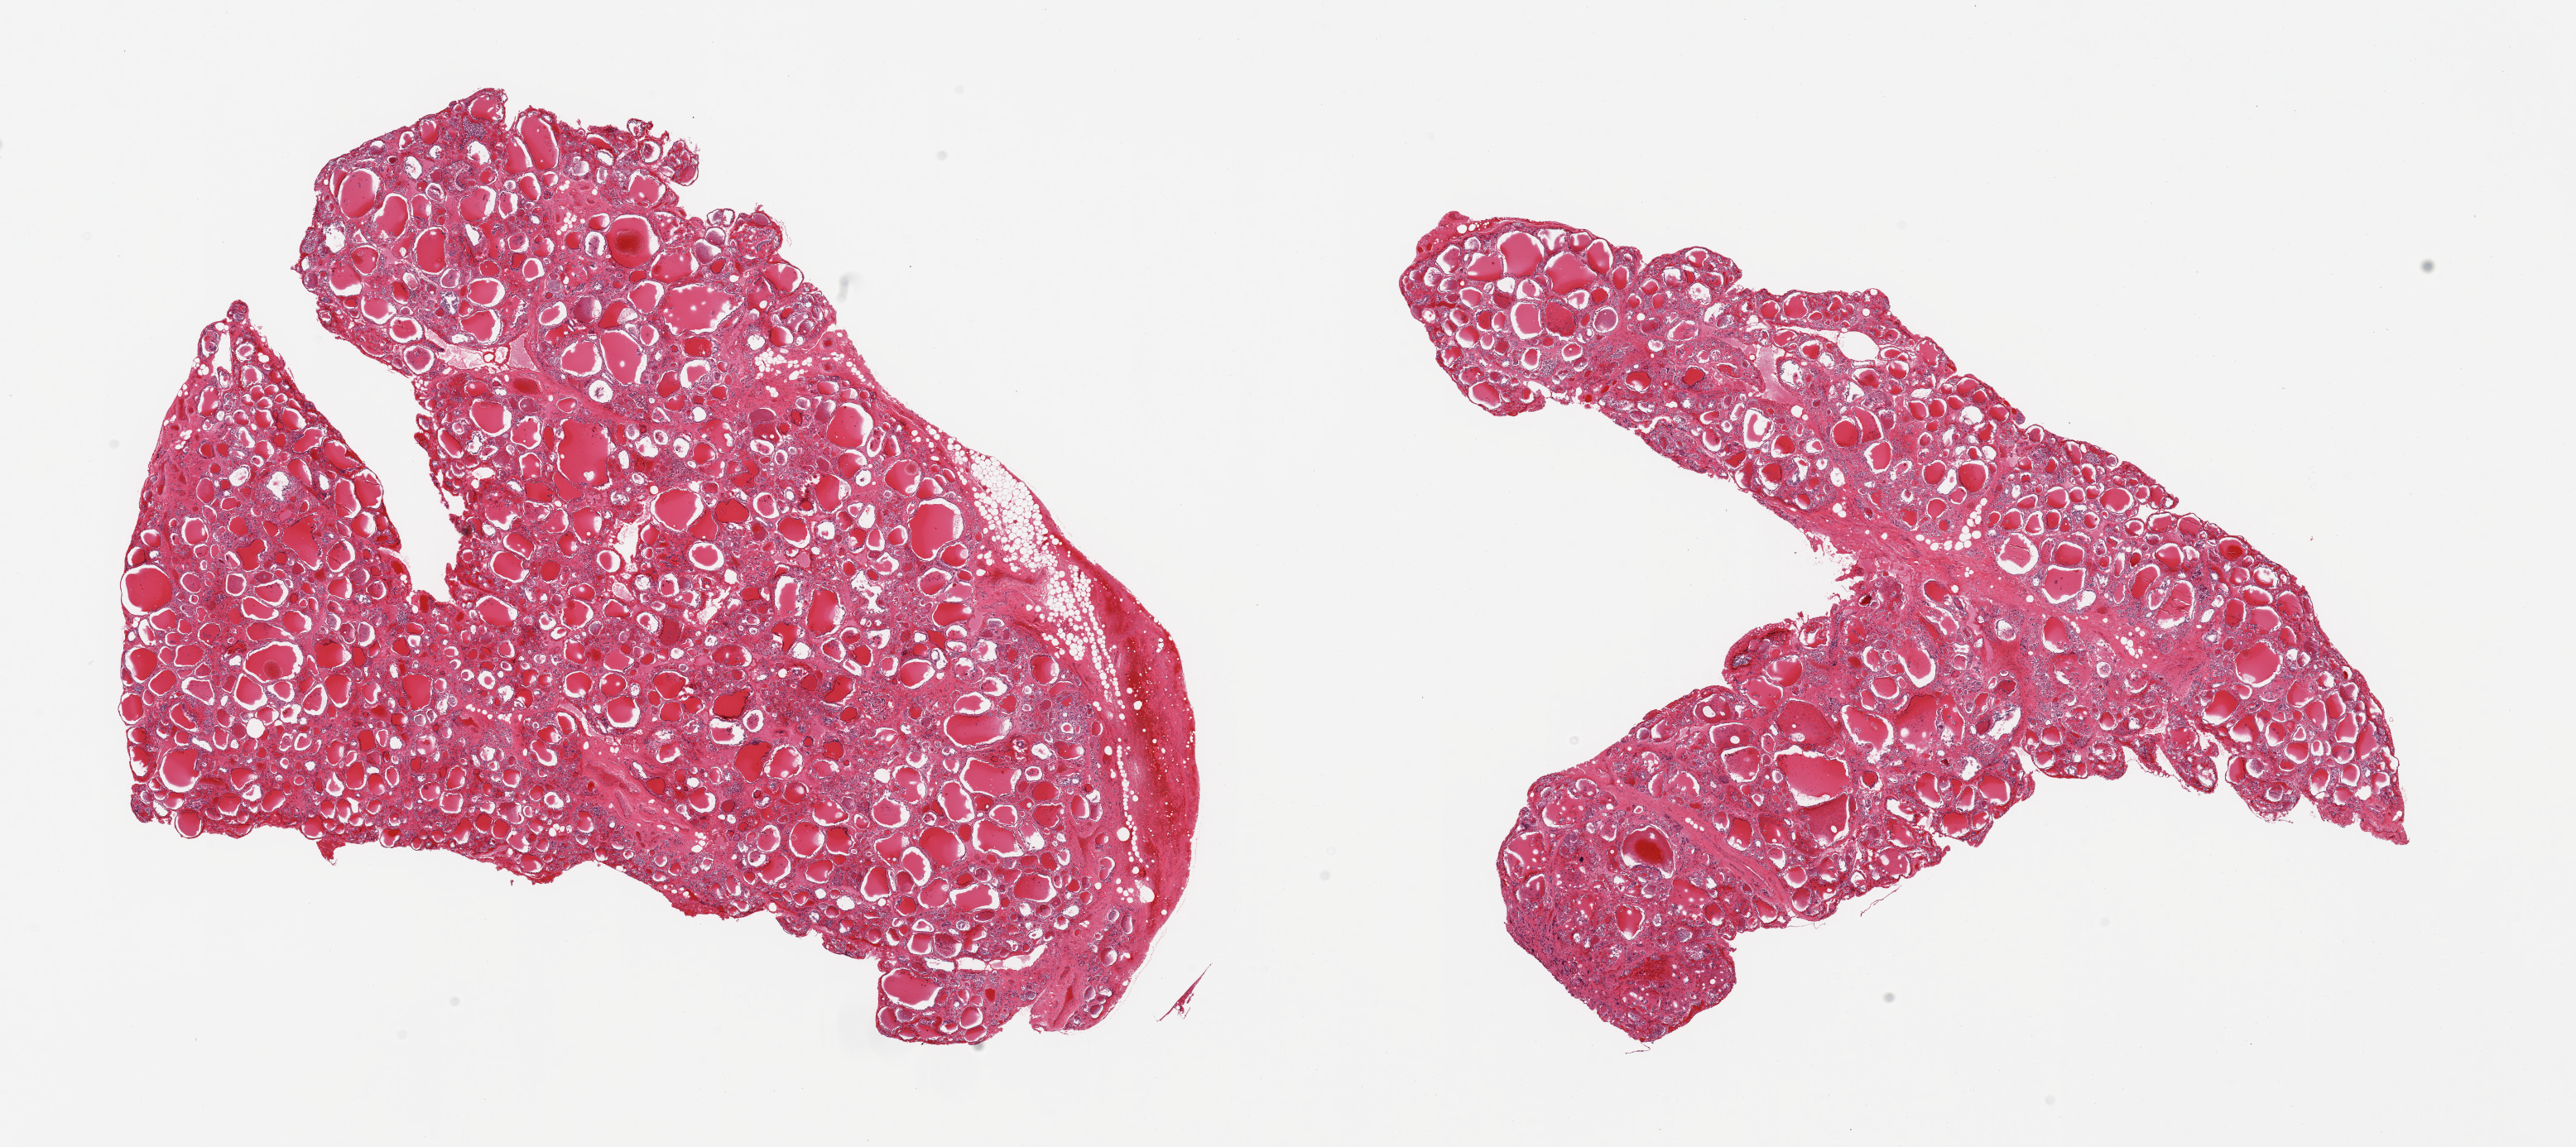
Digitized H&E-stained section — whole scanned area (about 24.6 x 11.0 mm, slide scanned at 20x) shown as a low-resolution overview; PAXgene-fixed, paraffin-embedded tissue; sampled site (target tissue): thyroid; donor tissue sample. Donor: male.
- review note (as recorded): 2 pieces; mild to moderate interstitial fibrosis